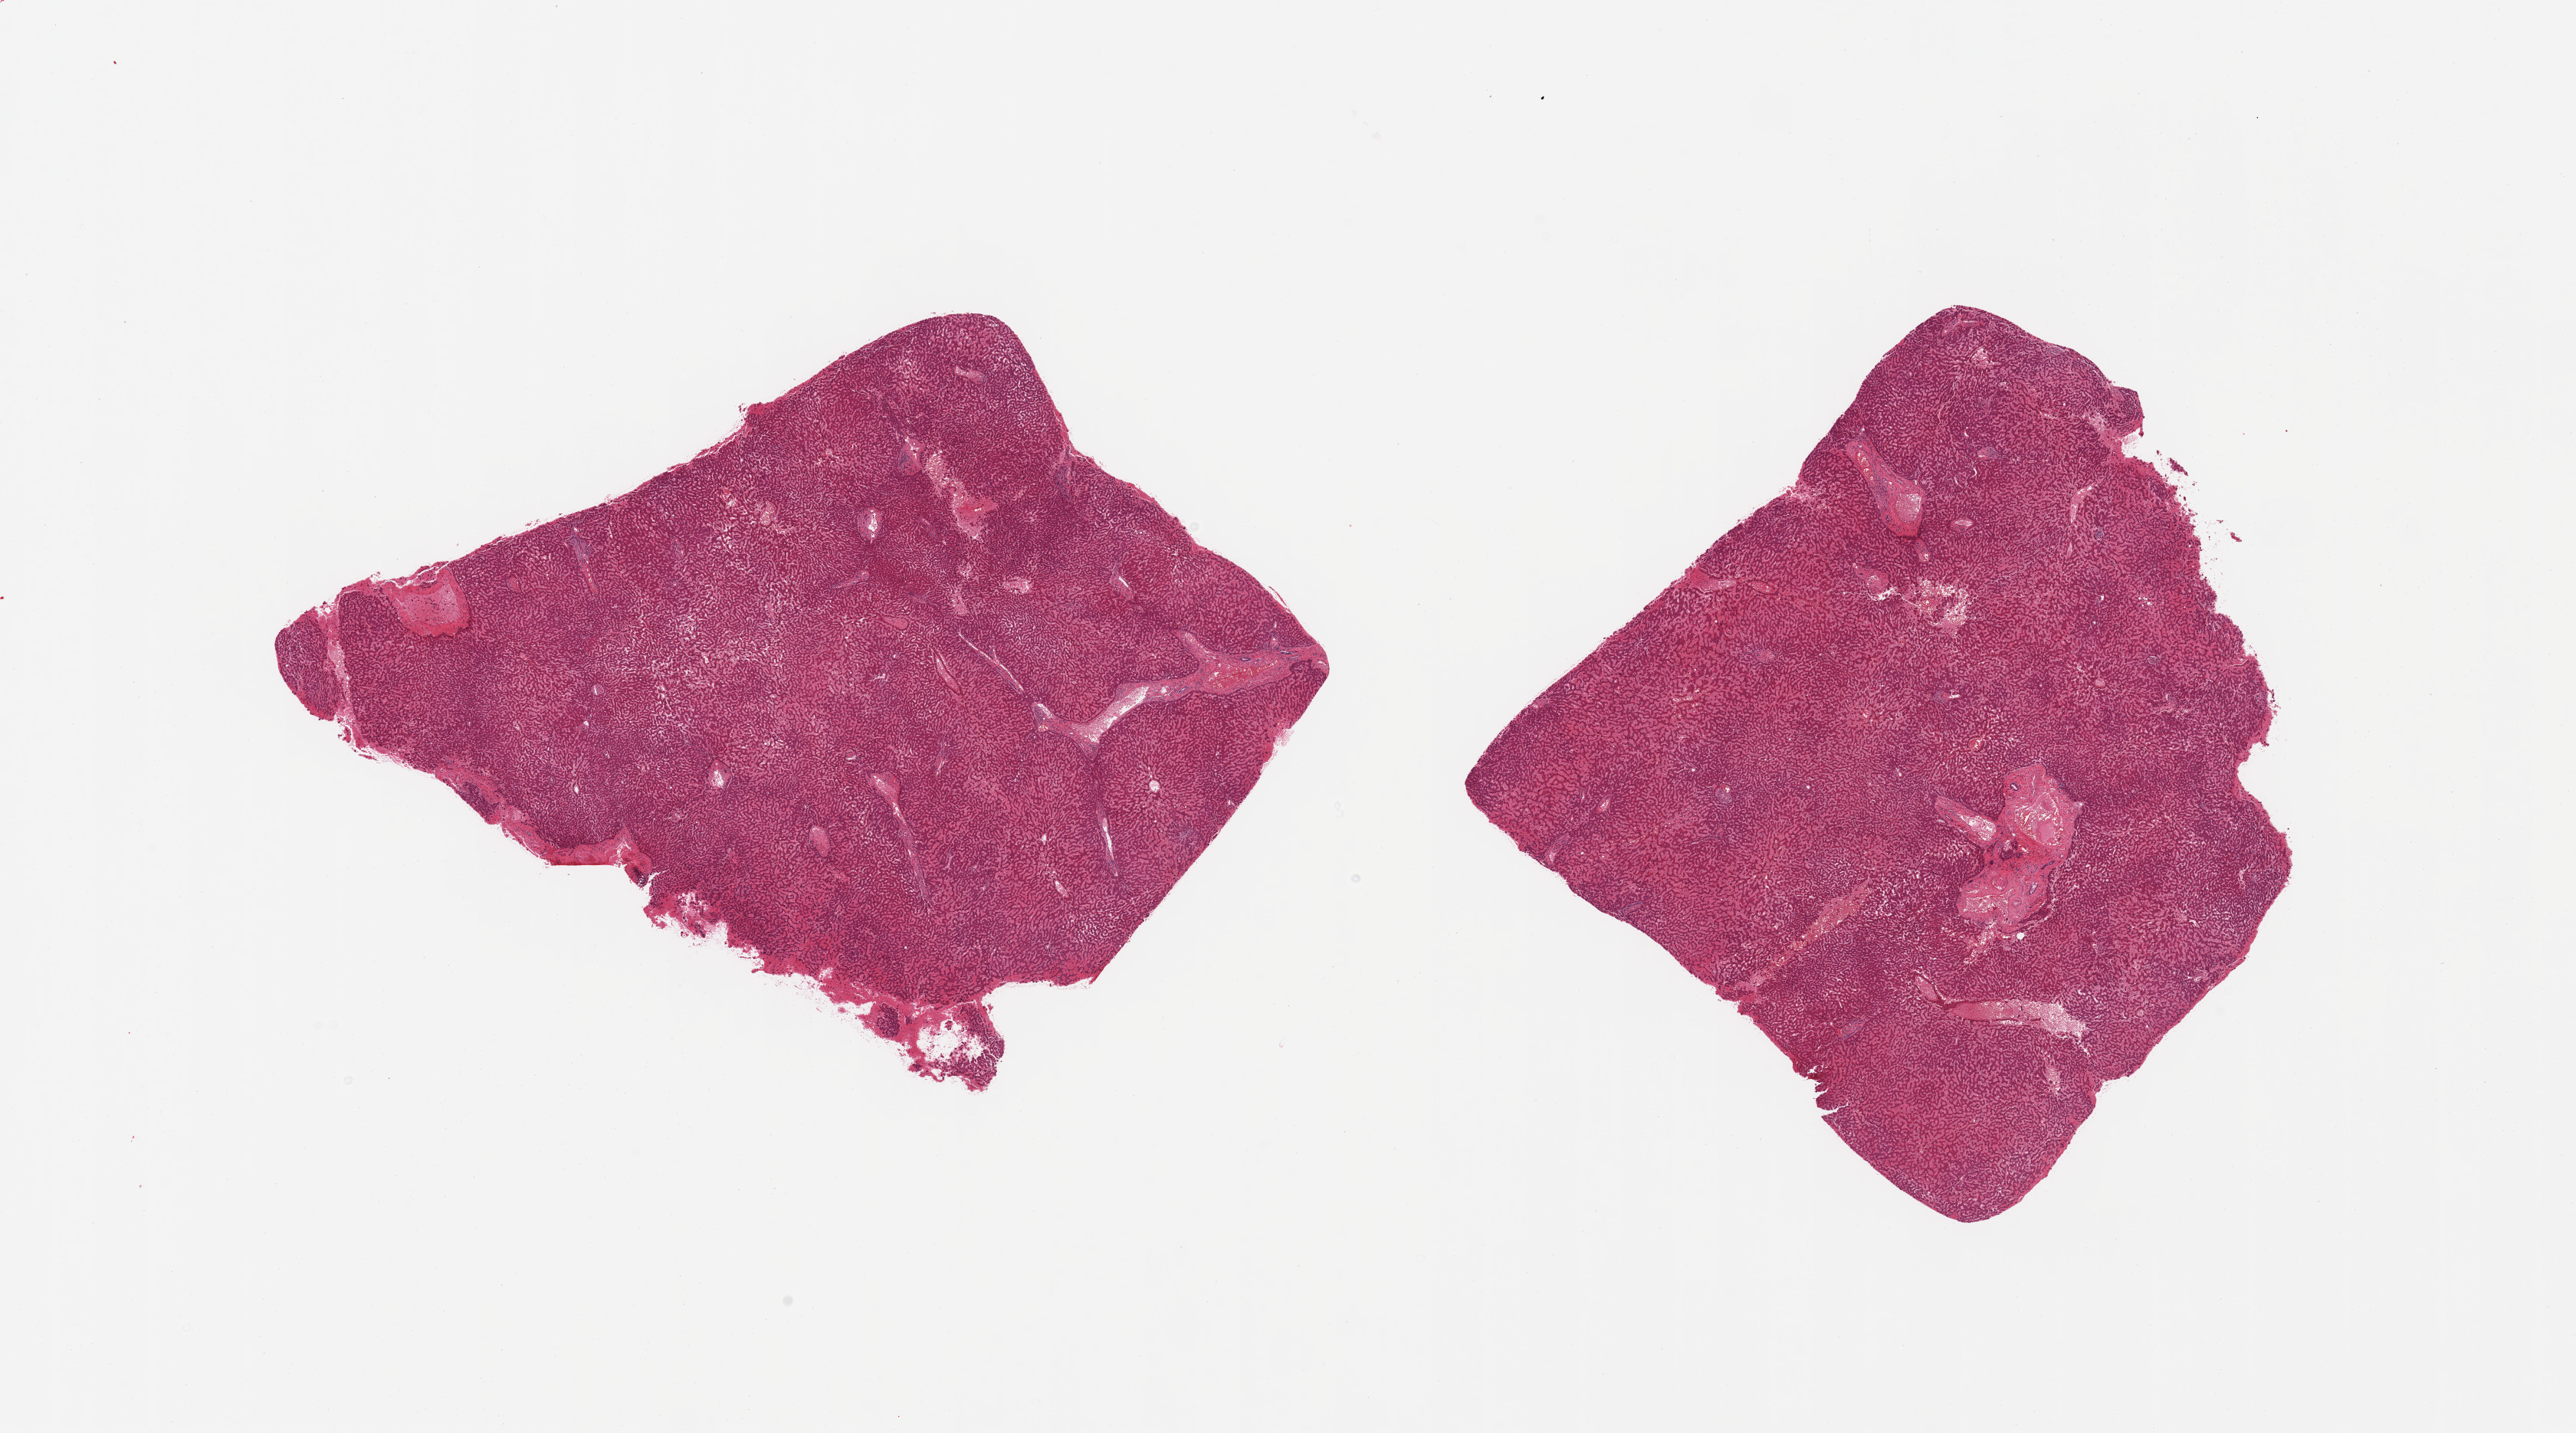
Digitized haematoxylin and eosin-stained section — a low-resolution overview of the entire scanned area, about 26.6 x 14.8 mm (from a 20x scan); PAXgene-fixed paraffin-embedded (PFPE) section; sampled site (target tissue): liver; donor tissue sample. Male donor.
Reviewer comment on this tissue sample: 2 pieces; moderate sinusoidal congestion.